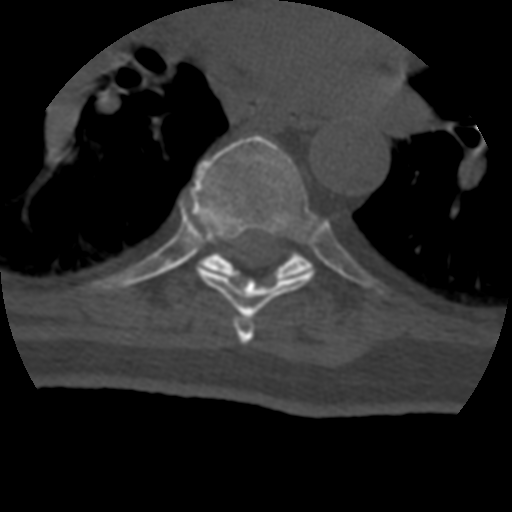
CT including the spine, one axial slice; slice 274 of 399 in the series (ordered by position); reconstruction kernel STANDARD; bone window (W 1800 / L 400 HU); 1.25 mm slice thickness; 512 × 512 image matrix, field of view 160 × 160 mm. Patient age 69 years. From the clinical record (not read from this slice): primary cancer: prostate.
Structures marked on this image (semi-automatic segmentation, software-assisted and operator-edited):
- T6 vertebra: bounding box (x1, y1, x2, y2) in pixels: (233, 318, 255, 344)
- T7 vertebra: (186, 135, 322, 319)
- T8 vertebra: (201, 251, 312, 281)